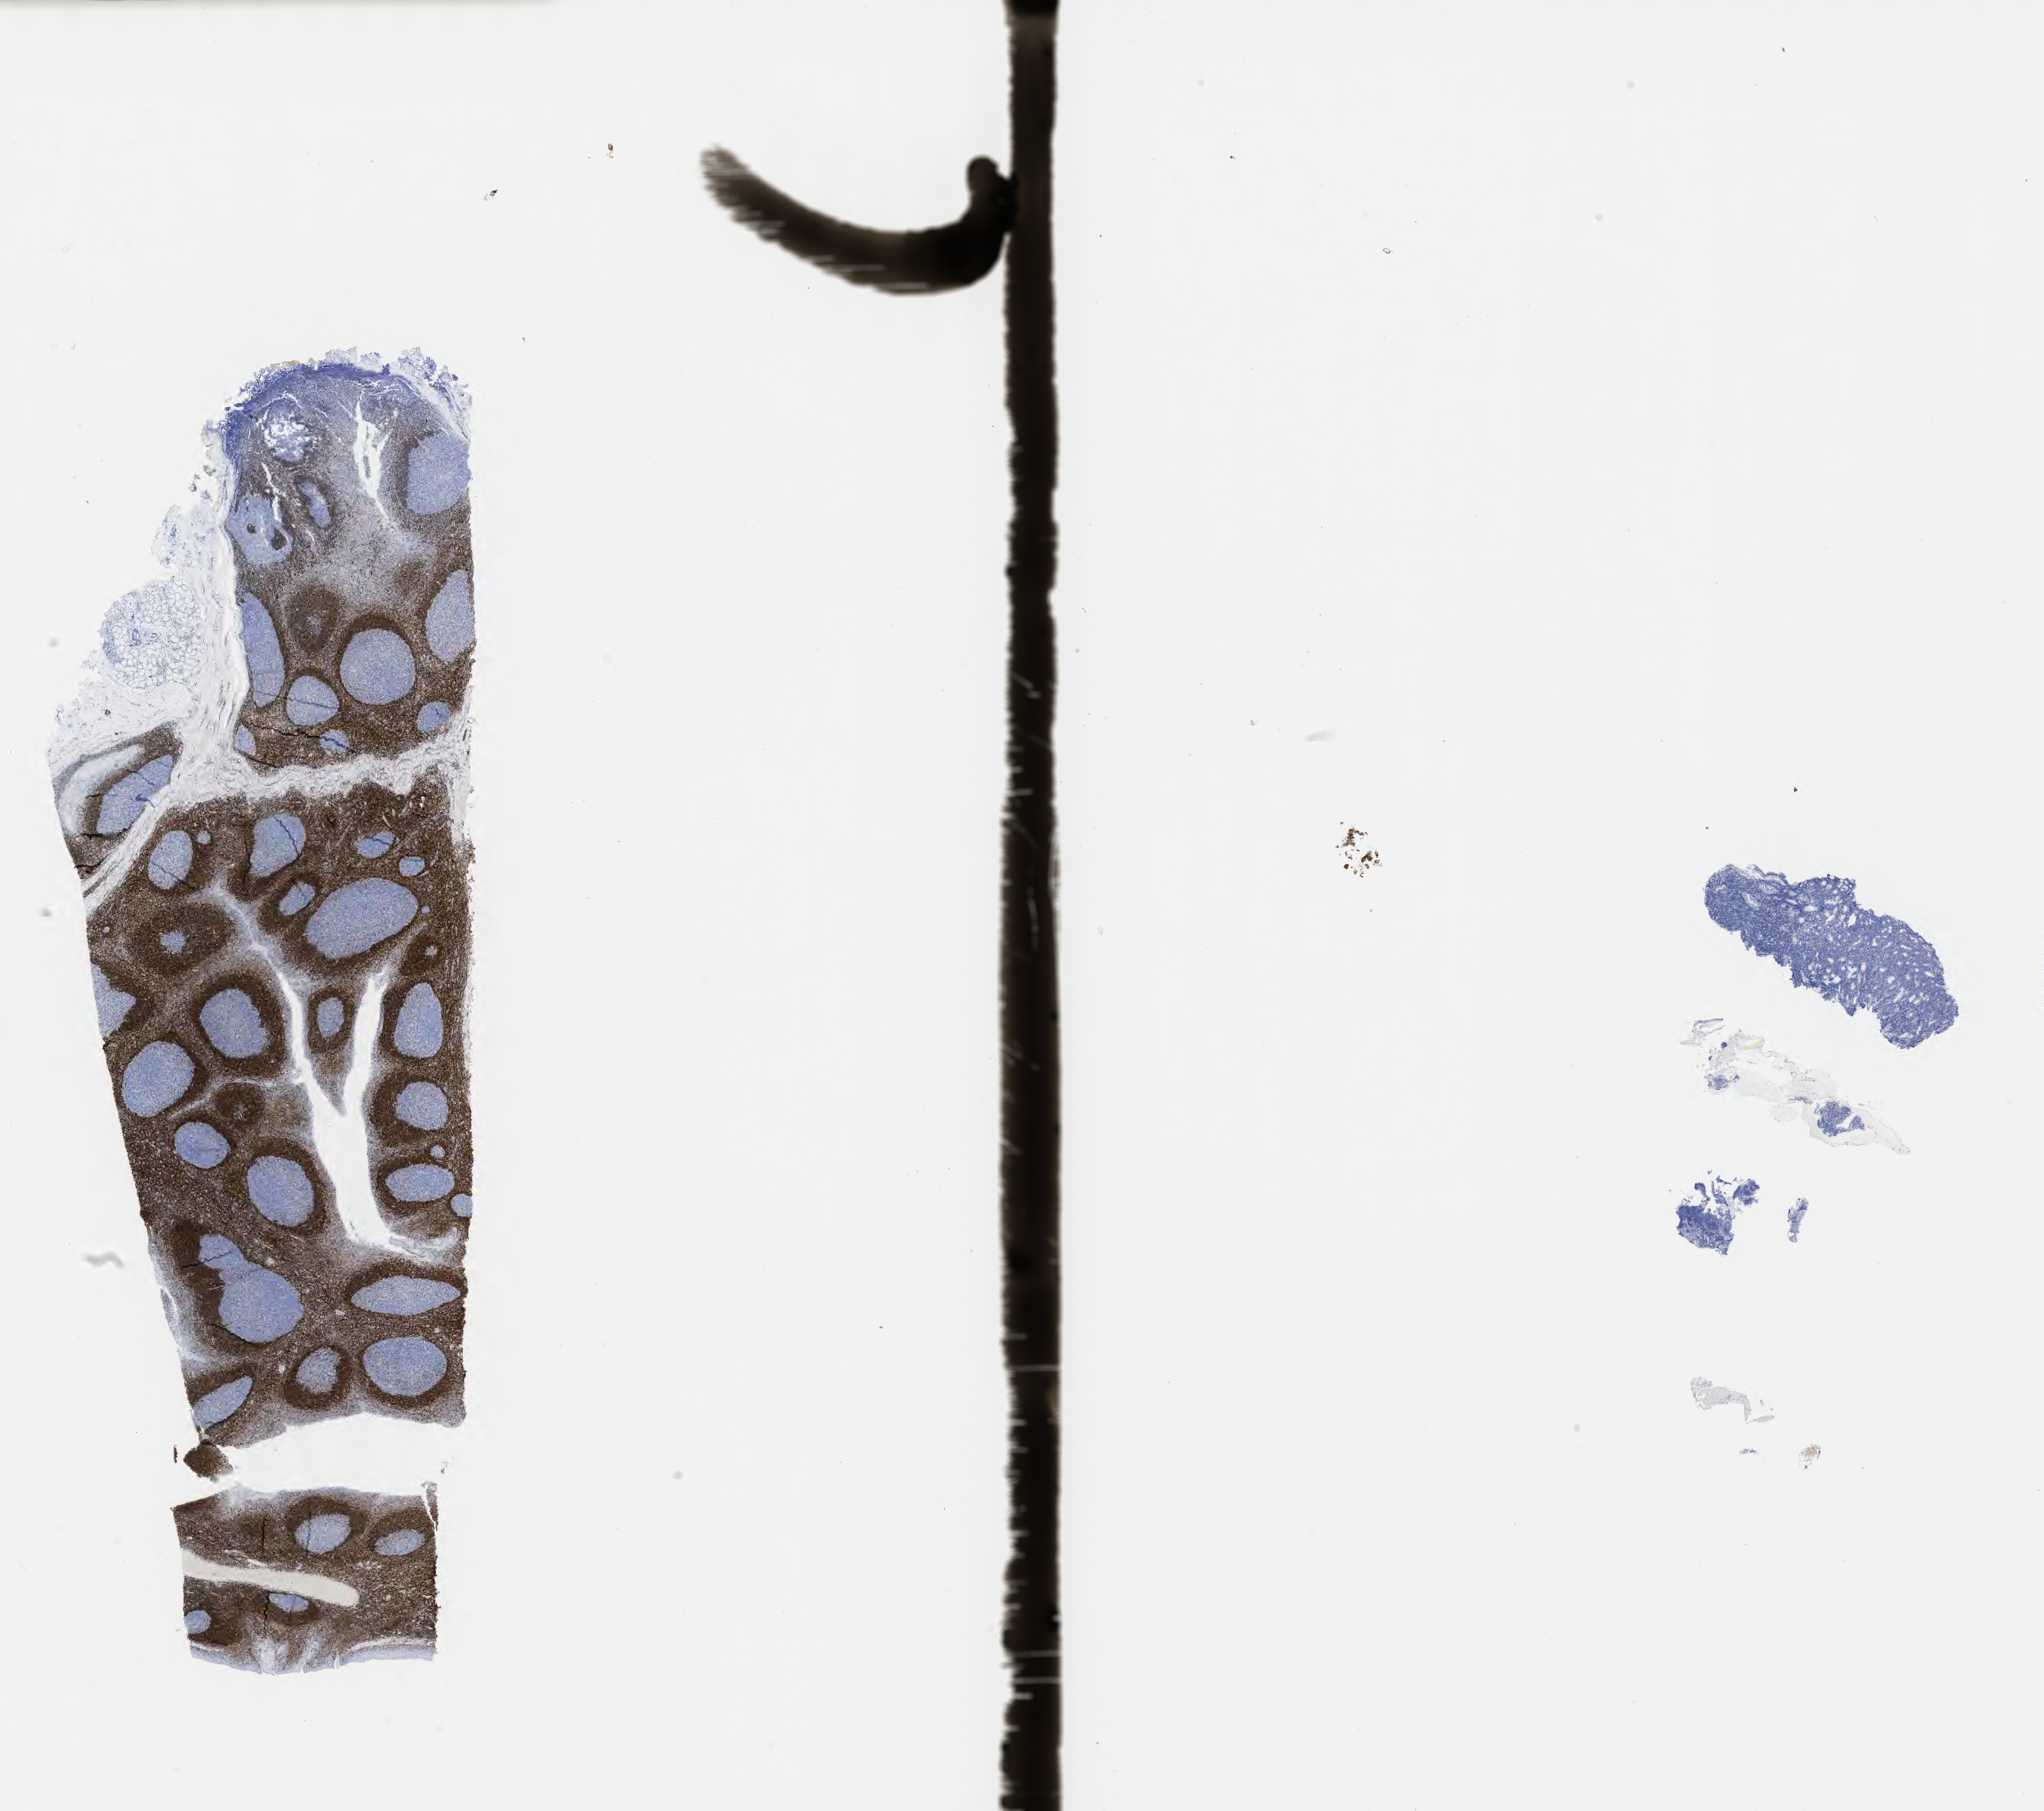
IHC for BCL2, whole-slide image, whole scanned area (about 21.6 x 19.2 mm) shown as a low-resolution overview, specimen: tumor tissue, anatomic site: stomach. Female patient, aged 28.
* histologic diagnosis: Burkitt lymphoma, NOS